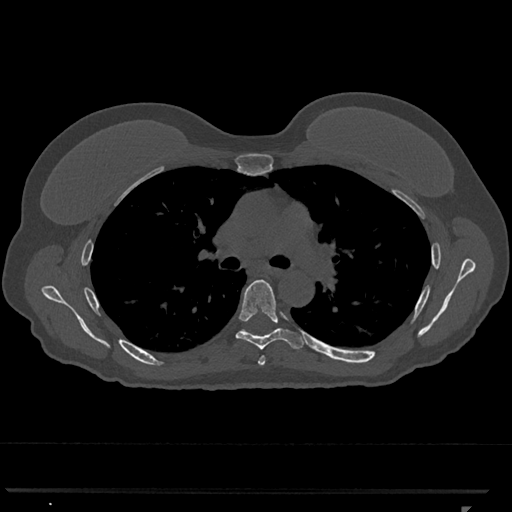
CT including the spine, one axial slice. Slice 762 of 793 in the series (ordered by position). Reconstruction kernel Br40s/3. 120 kVp. Bone window (W 1800 / L 400 HU). 0.5 mm slice thickness. 512 × 512 image matrix. Patient: female, 62 years. From the clinical record (not read from this slice): primary cancer: renal.
Structures marked on this image (semi-automatically segmented with operator editing):
- T5 vertebra: bounding box <258,356,265,366> (left, top, right, bottom; pixels)
- T6 vertebra: <235,279,305,350>